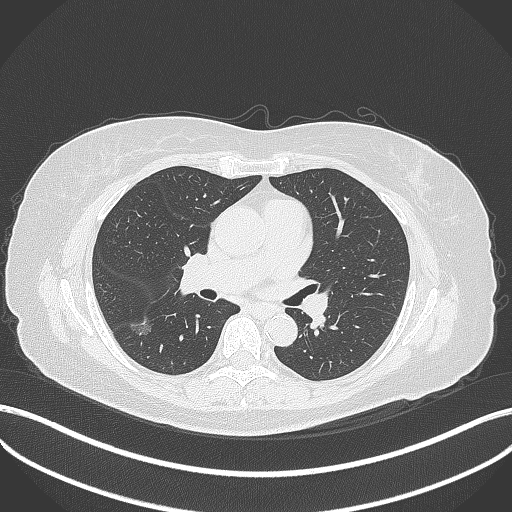
Chest CT, one axial slice; slice 177 of 322 in the series (ordered by position); lung window (W 1500 / L -600 HU); 1 mm slice thickness; 512 × 512 image matrix. Female patient, age 64 years. Case-level facts recorded for this patient, not image findings: clinical TNM (as recorded): T1c N0 M0.
Outlined on this slice (bounding box drawn by a radiologist):
- lung tumour (recorded histology: adenocarcinoma): bounding box <130,314,155,339> (left, top, right, bottom; pixels)